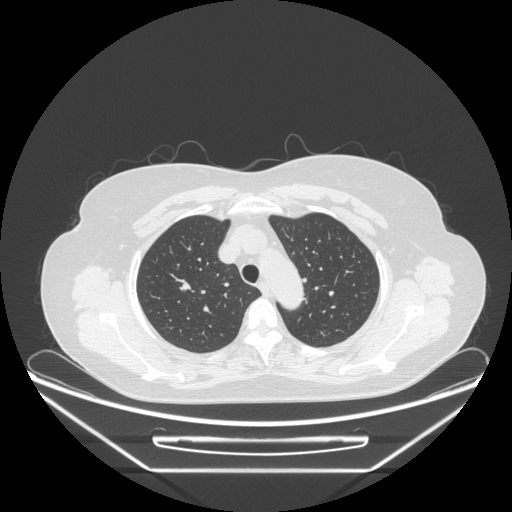
Chest CT, one axial slice; position 192 of 236 along the scan axis; reconstruction kernel STANDARD; 120 kVp; lung window (W 1500 / L -600 HU); 1.25 mm slice thickness; 512 × 512 image matrix, field of view 433 × 433 mm. Patient: female, 60 years. From the clinical record (not read from this slice): clinical TNM (as recorded): T1c N0 M0.
Structures marked on this image (rectangle marked by the reading radiologist):
- lung tumour (recorded histology: adenocarcinoma): bounding box [x1, y1, x2, y2] px = [176, 277, 194, 300]